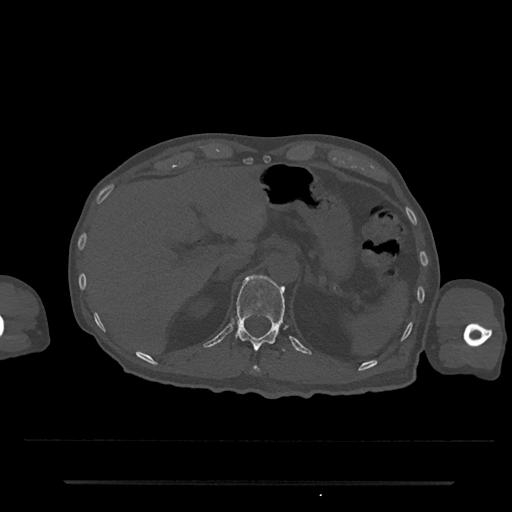
CT including the spine, one axial slice; position 195 of 797 along the scan axis; reconstruction kernel Br40s/3; 120 kVp; bone window (W 1800 / L 400 HU); 0.5 mm slice thickness; 512 × 512 image matrix. Patient: male, 74 years. Case-level facts recorded for this patient, not image findings: primary cancer: prostate.
Annotated regions visible in this slice (semi-automatically segmented with operator editing):
- T11 vertebra: box from (x=252, y=365) to (x=260, y=373) px
- T12 vertebra: (x=235, y=277)–(x=286, y=351)